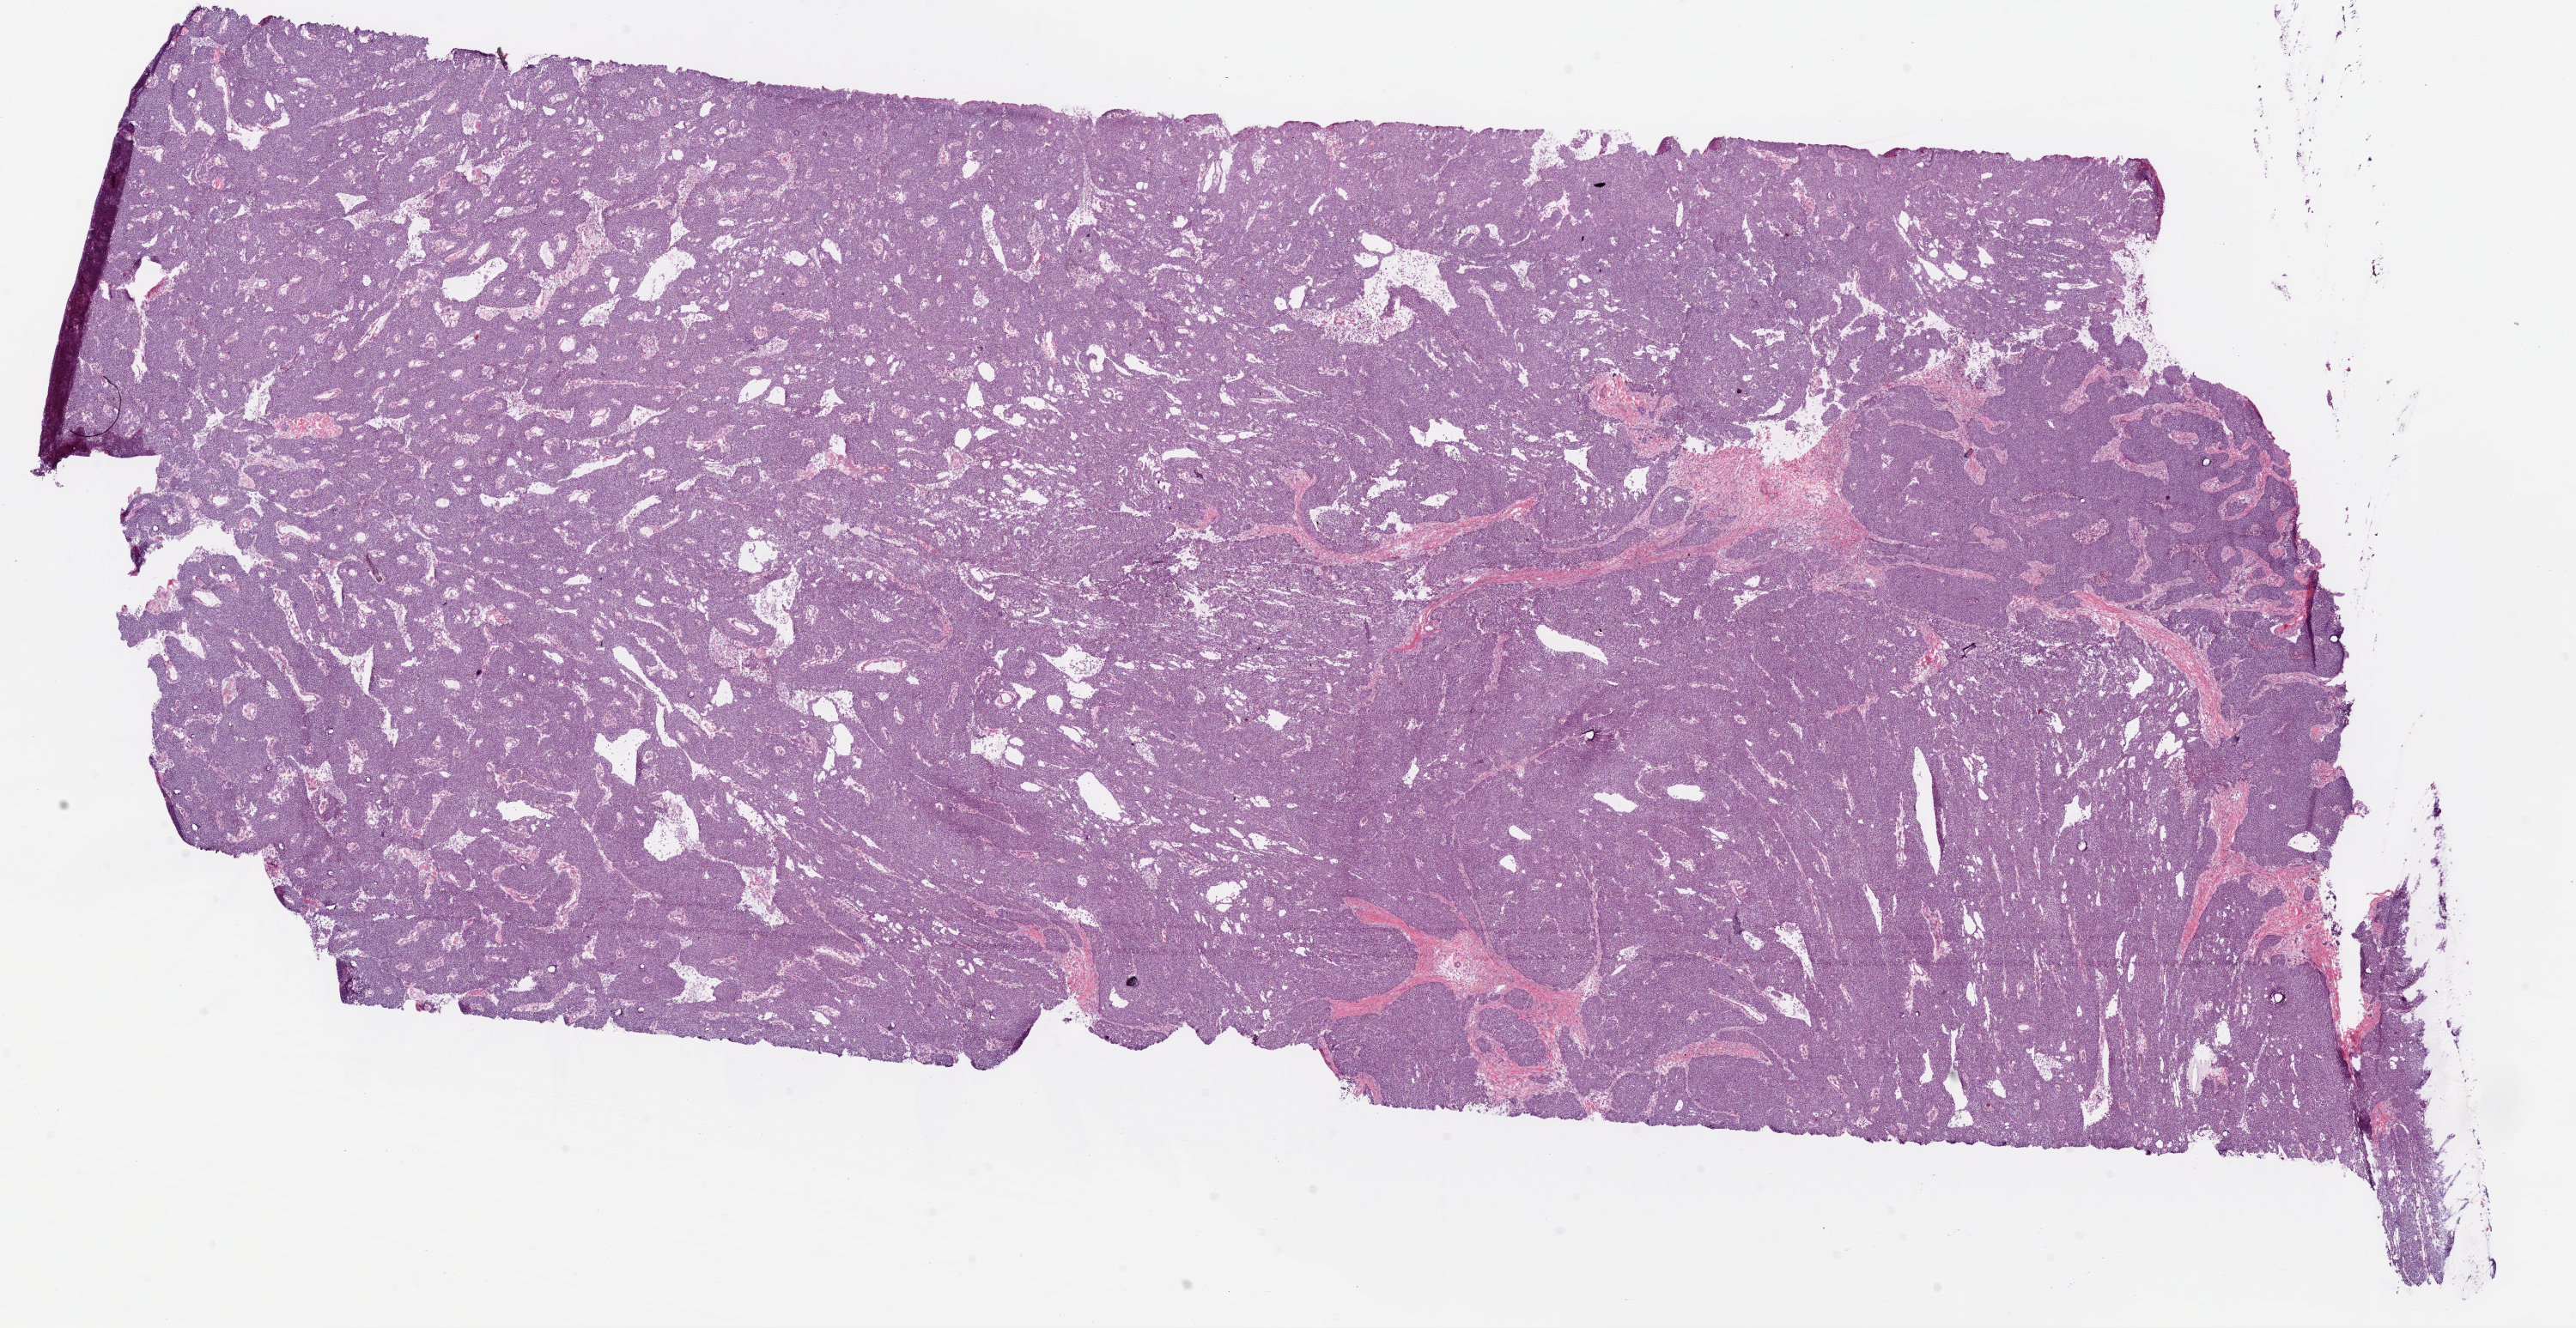
H&E-stained whole-slide image, a low-resolution overview of the entire scanned area, about 24.1 x 12.4 mm (slide scanned at 20x), frozen section, sample: primary tumour, ovary. Patient: female, age at initial diagnosis 38 years. Histologic grade: G3 (poorly differentiated). Composition of this section per pathologist review: tumour cells 90%, tumour nuclei 85%, normal cells 0%, stromal cells 5%, necrosis 5%.
• diagnosis: Serous cystadenocarcinoma, NOS
• laterality: bilateral
• FIGO stage: IIIC